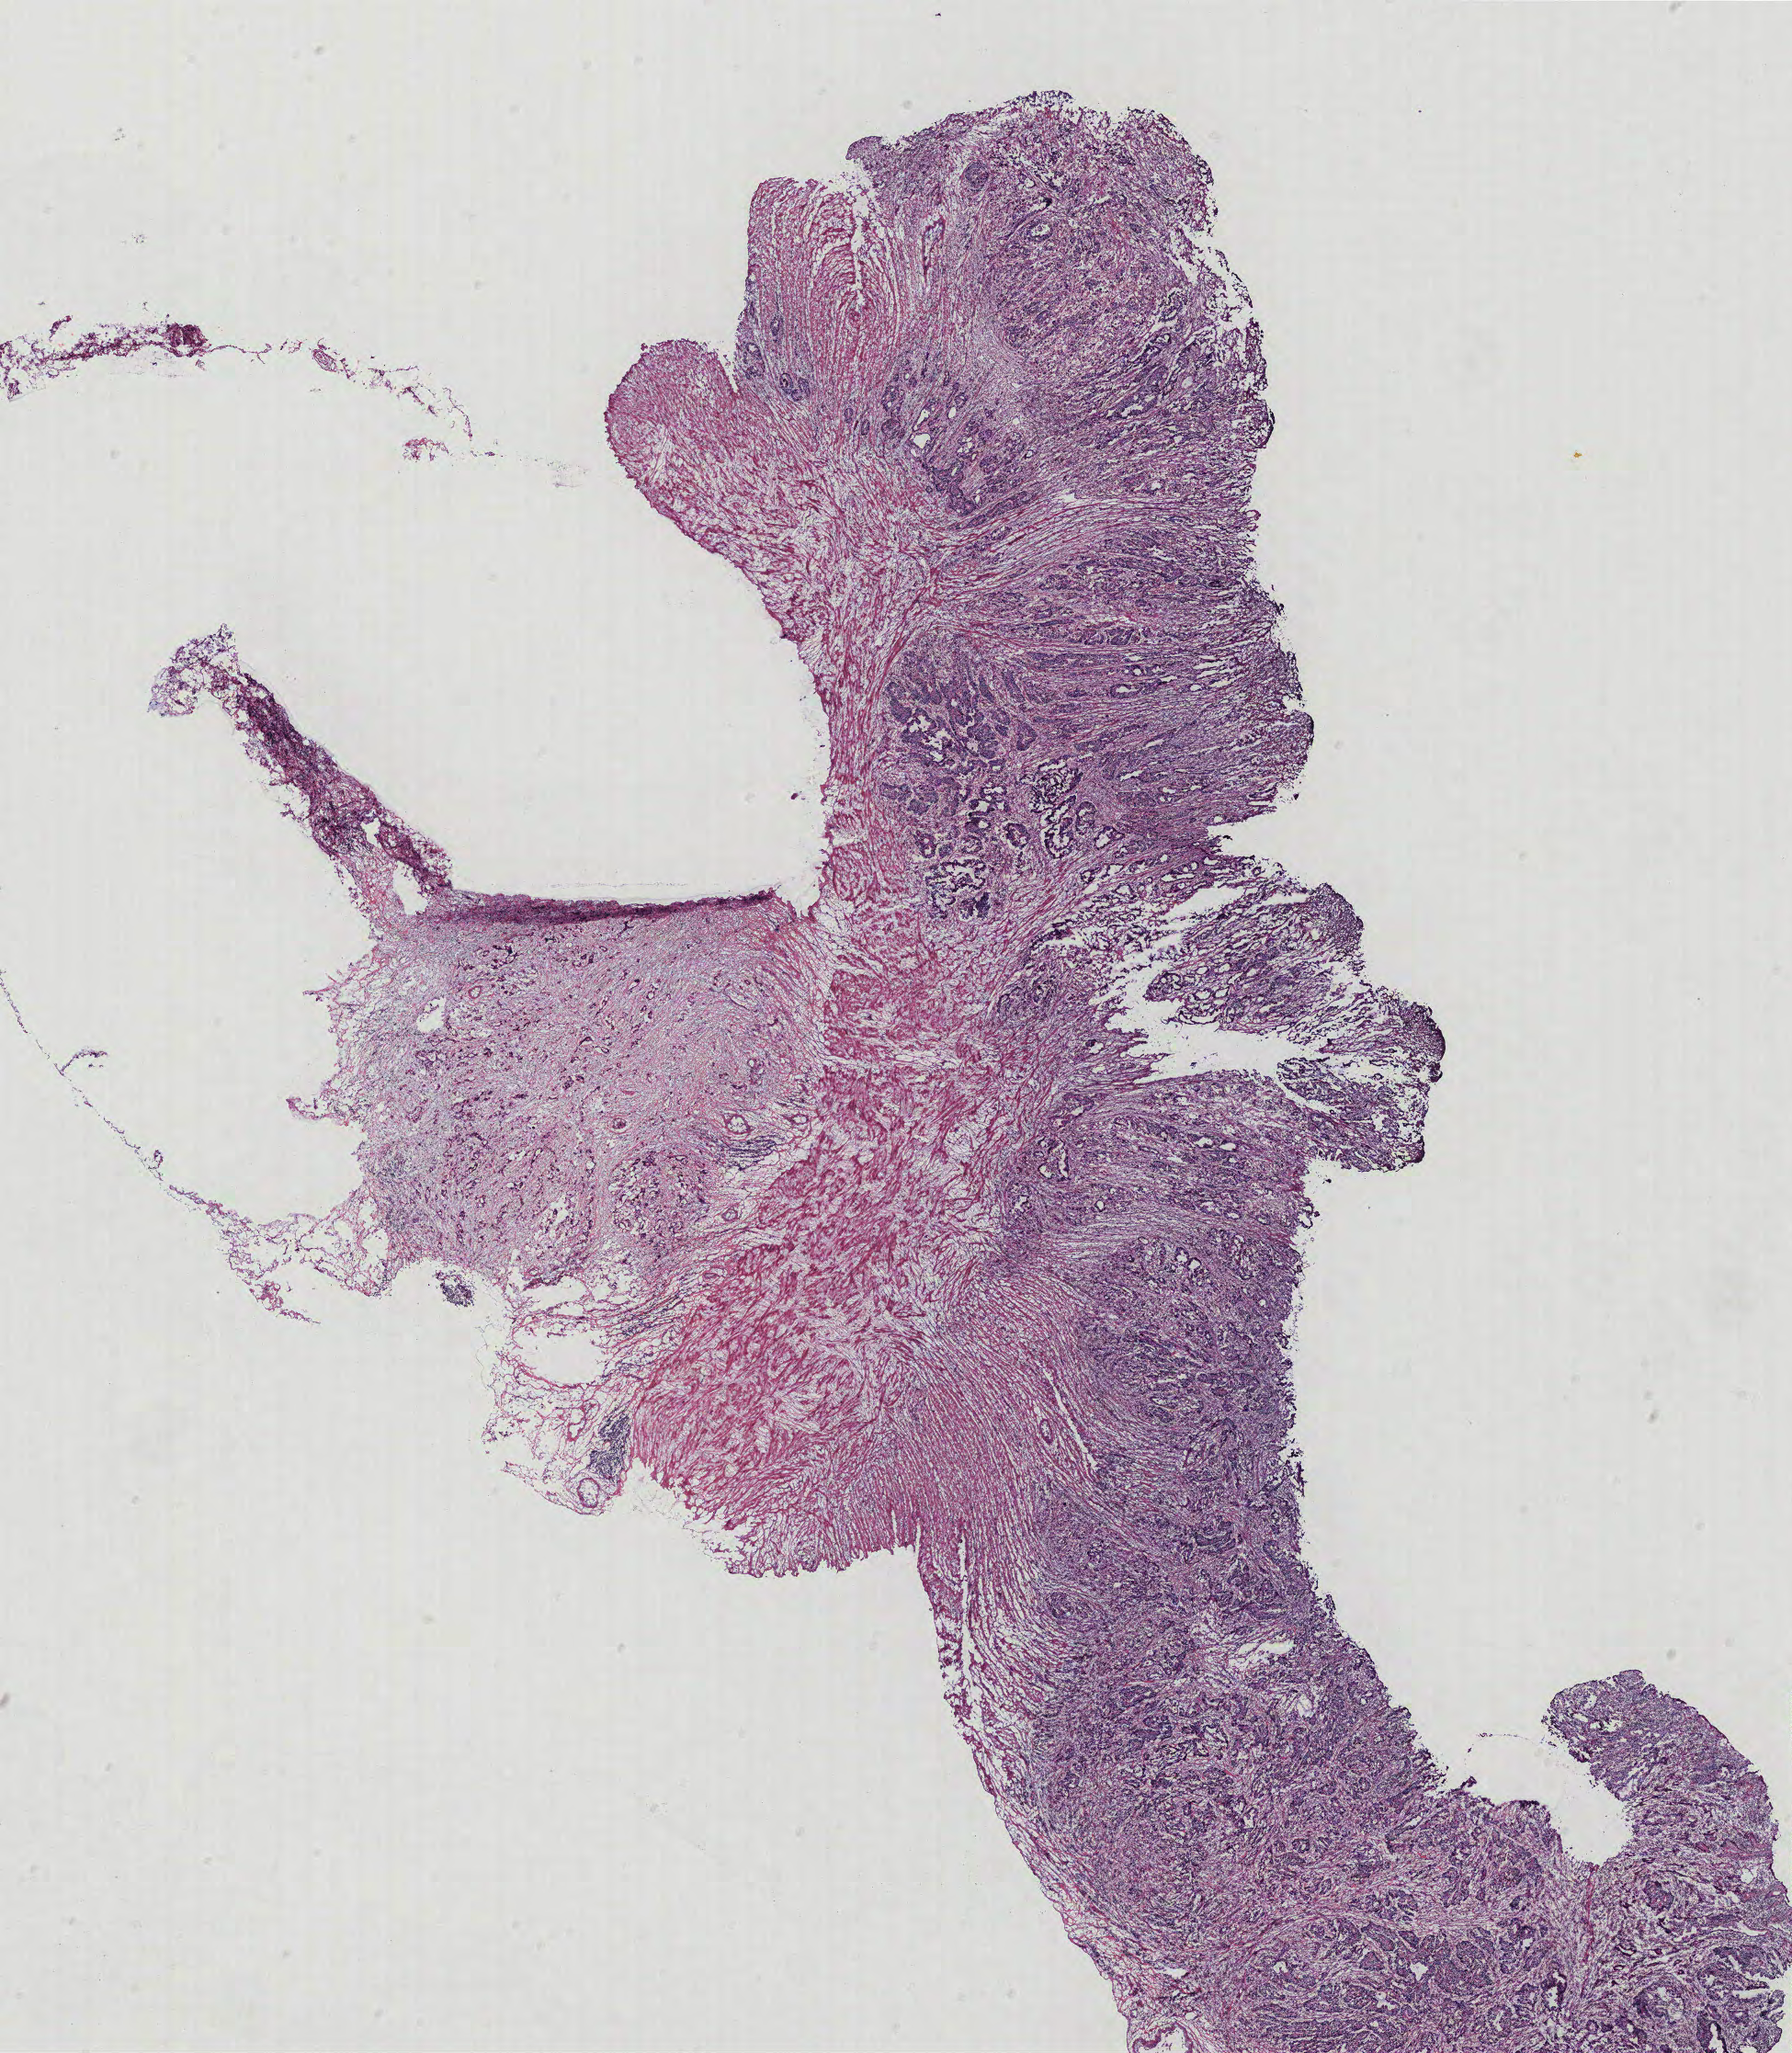
H&E-stained whole-slide image, low-resolution overview of the scanned area, about 15.6 x 17.9 mm (from a 40x scan). Tumour tissue sample, colon. Patient: female, age 71 years.
* primary tumour site (as recorded): colon
* histologic diagnosis: Adenocarcinoma, NOS
* AJCC pathologic stage: IIIB